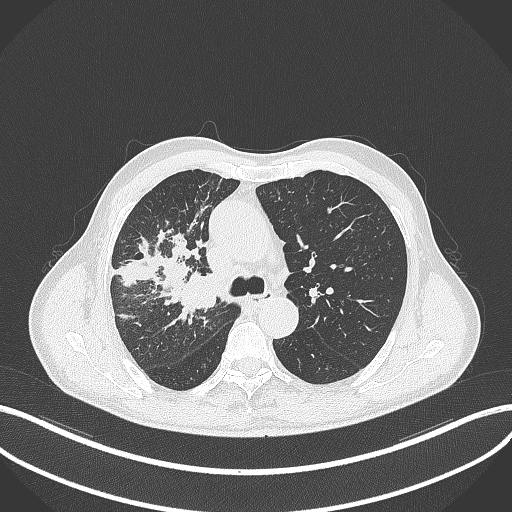
Chest CT, one axial slice. Position 328 of 490 along the scan axis. Lung window (W 1500 / L -600 HU). 512 × 512 image matrix. Patient: male, 69 years. From the clinical record (not read from this slice): clinical TNM (as recorded): T2a N0 M0.
Annotated regions visible in this slice (rectangle marked by the reading radiologist):
- lung tumour (recorded histology: adenocarcinoma): bounding box (x1, y1, x2, y2) in pixels: (183, 268, 218, 311)